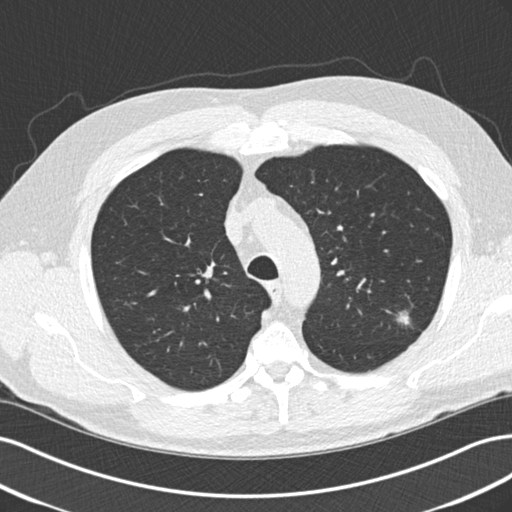
Low-dose screening chest CT, axial slice, second annual screen, lung window (W 1500 / L -600 HU), standard (soft-tissue) reconstruction kernel (B30f), slice 49 of 209 in the series, 512 × 512 image matrix, field of view 360 × 360 mm. Male participant, aged 65 years at enrolment. Former smoker at enrolment.
Lesion marked by an expert reader, bounding box (x1, y1, x2, y2) in pixels: (386, 304, 424, 343). The exam's reader record, not a measurement of the box and not confirmed to be the same lesion: non-calcified nodule or mass ≥4 mm, left upper lobe, 10 × 9 mm, poorly defined margins, mixed attenuation, pre-existing on the prior screen: yes; interval growth: no. Later outcome: lung cancer diagnosed 221 days after this screen — adenocarcinoma, NOS, left upper lobe, poorly differentiated (G3), stage IA (AJCC 6th edition), 13 mm at pathology.